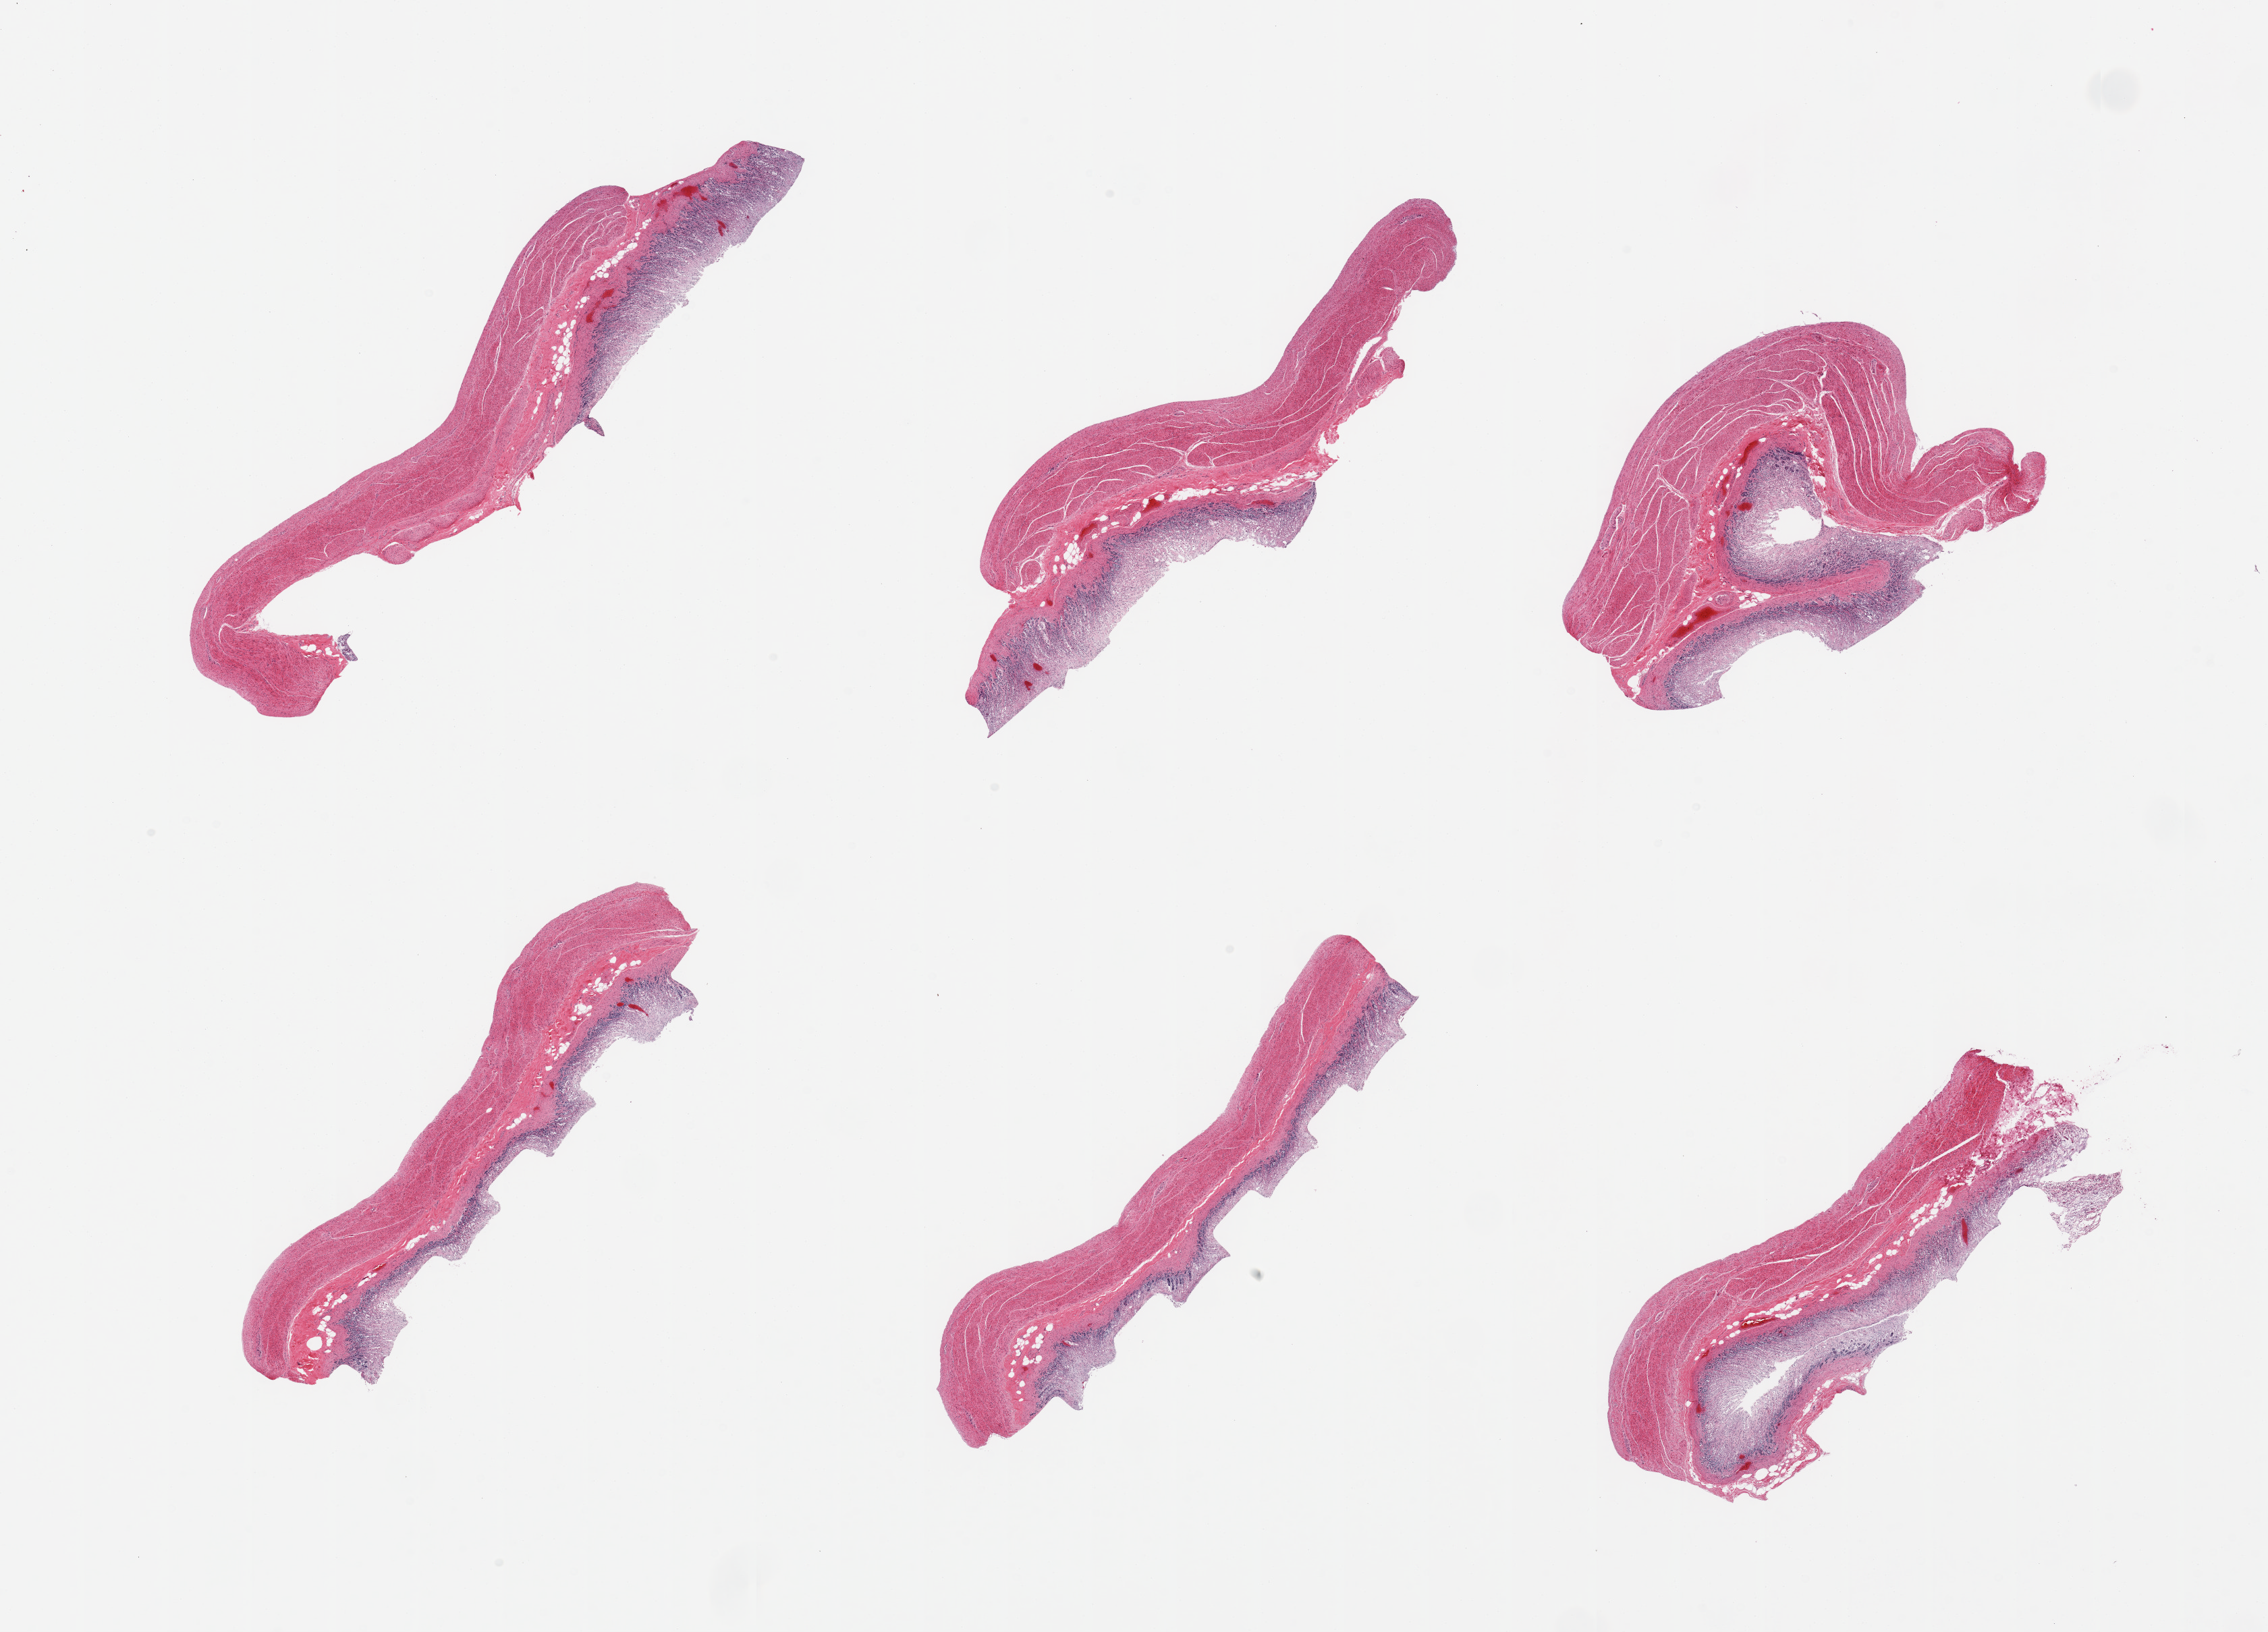
Whole-slide image, H&E stain — low-resolution overview of the scanned area, about 26.6 x 19.1 mm (slide scanned at 20x). PAXgene-fixed, paraffin-embedded tissue. Target tissue: stomach. Donor tissue sample. Donor: female.
- reviewer comment on this tissue sample: 6 pieces; totally autolyzed mucosa; intact muscularis